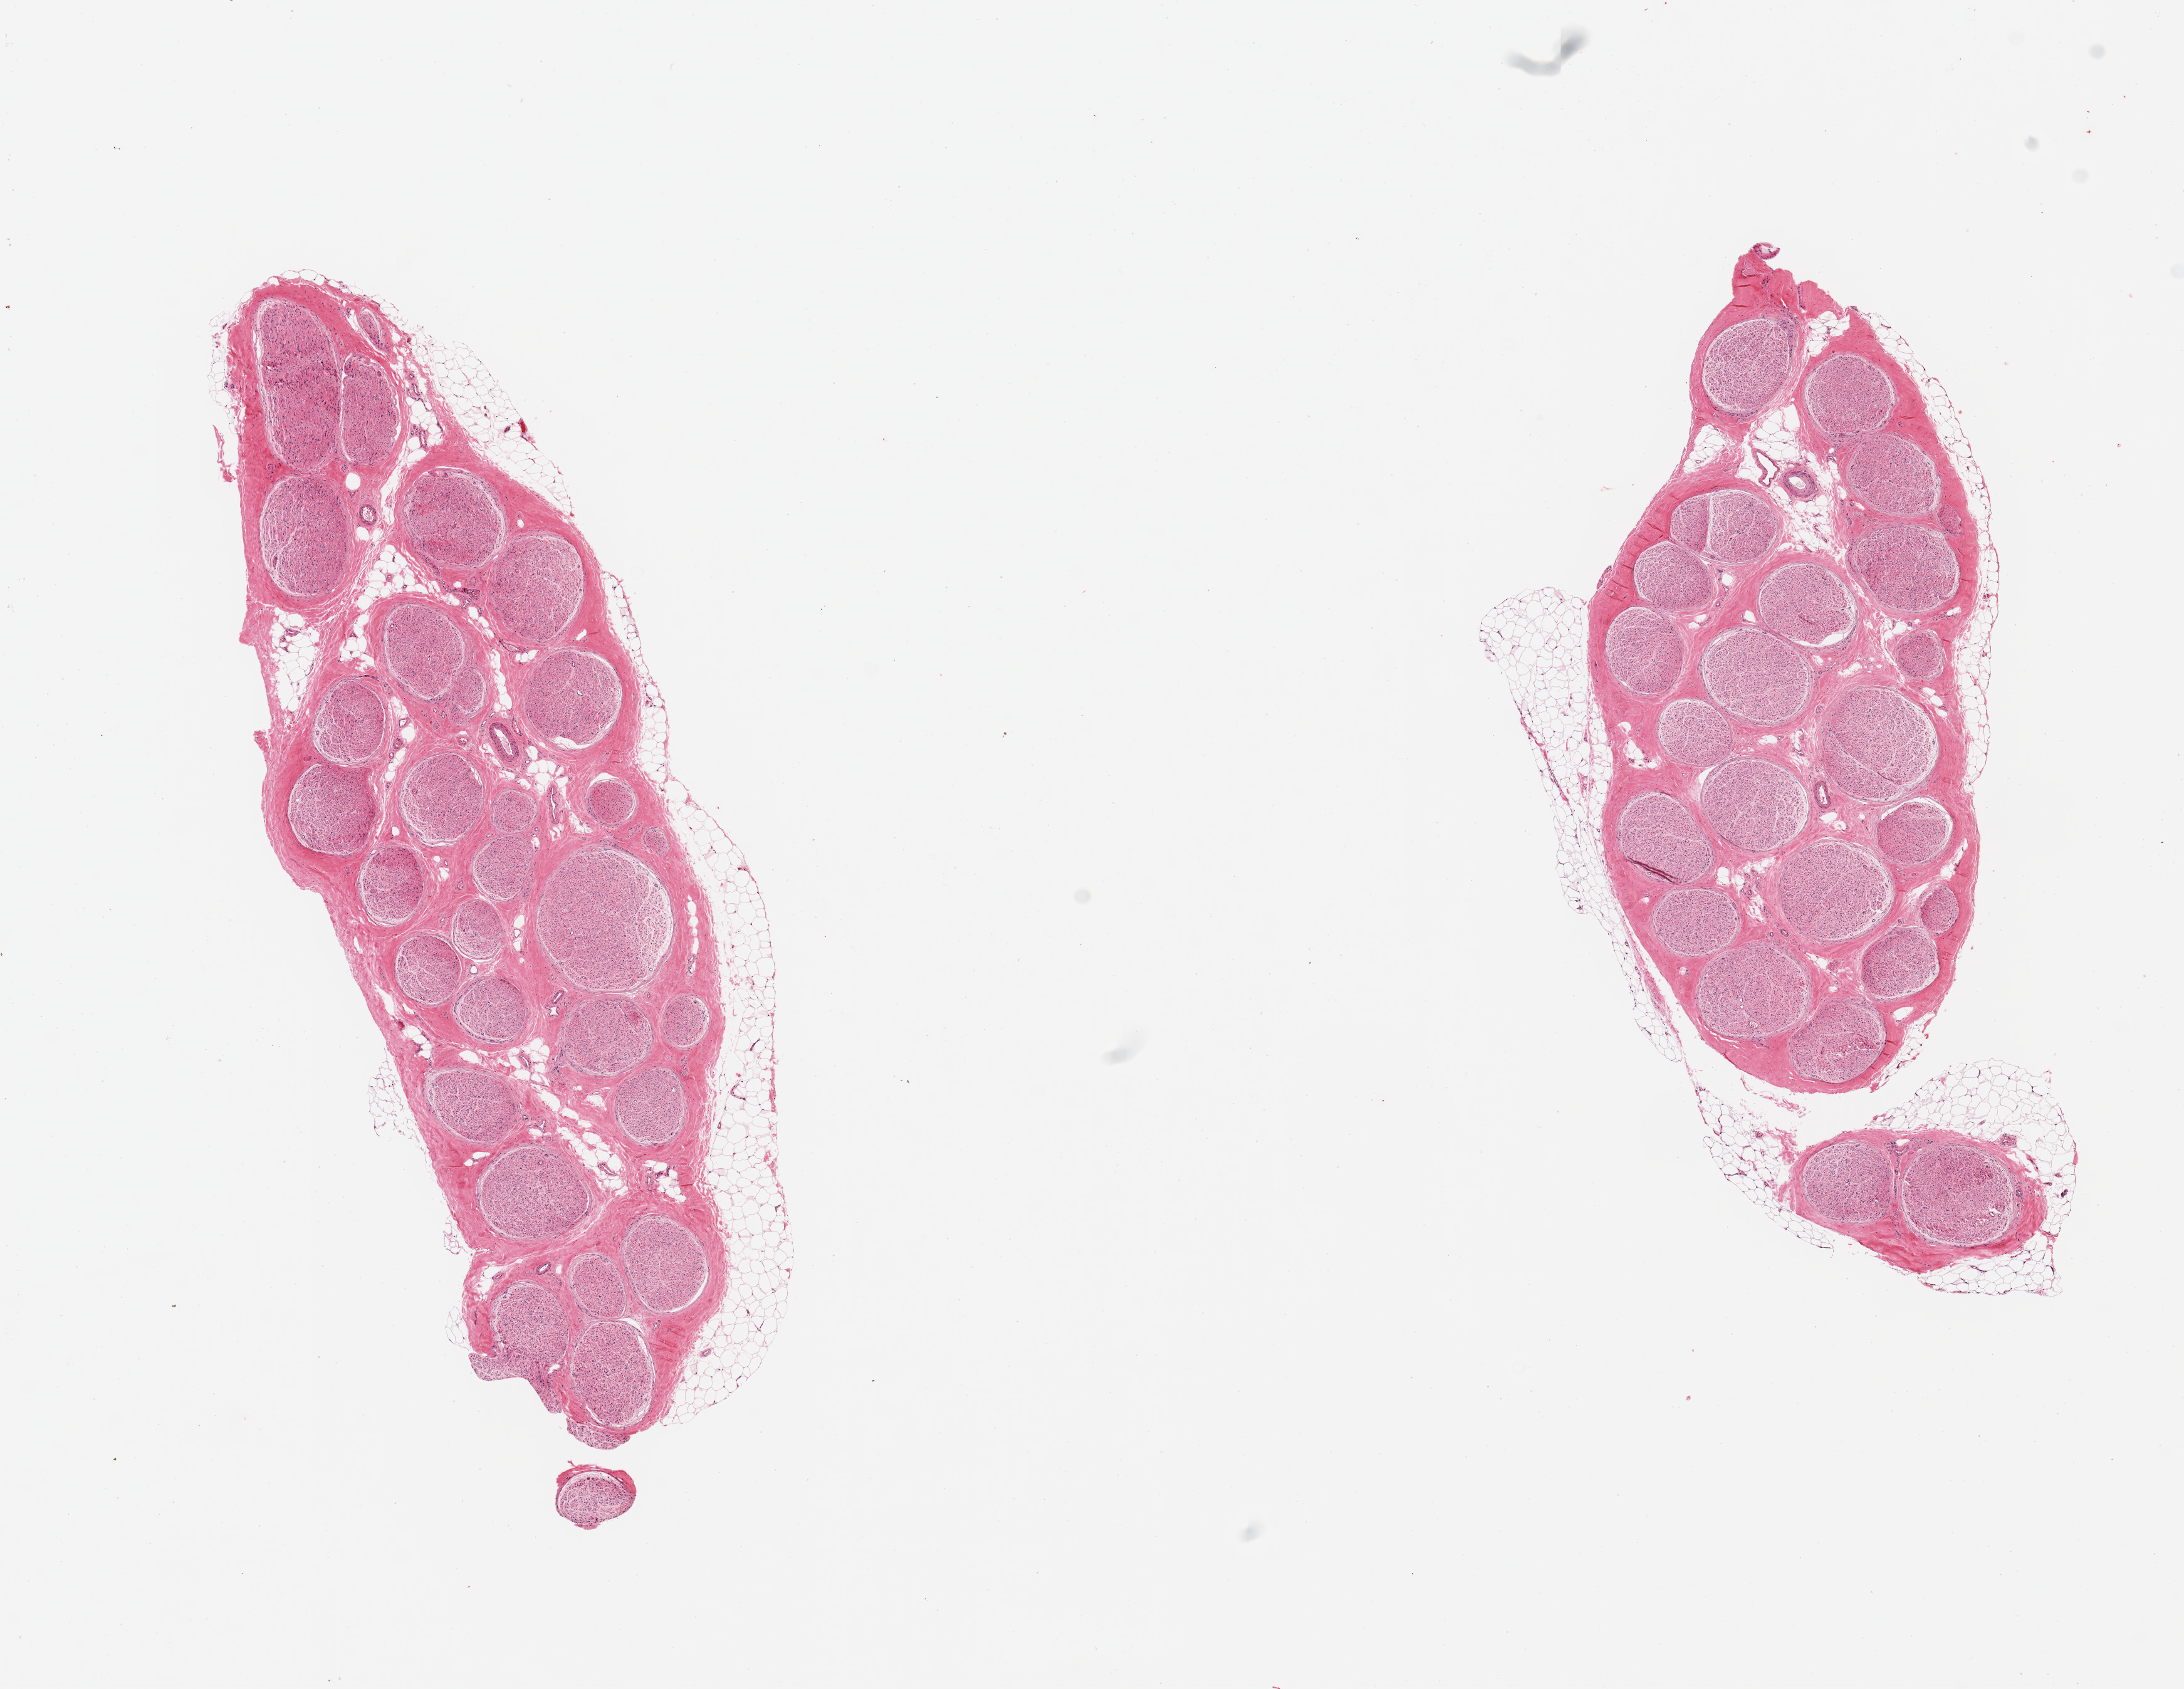
H&E whole-slide image, shown as a low-resolution overview of the whole scanned area (about 13.8 x 10.7 mm, from a 20x scan), PAXgene-fixed, paraffin-embedded tissue, target tissue: tibial nerve, tissue donor sample. Donor sex: male.
* pathologist's review note for this sample: 2 pieces; thin external coating of fat up to 0.7 mm; <5% internal fat